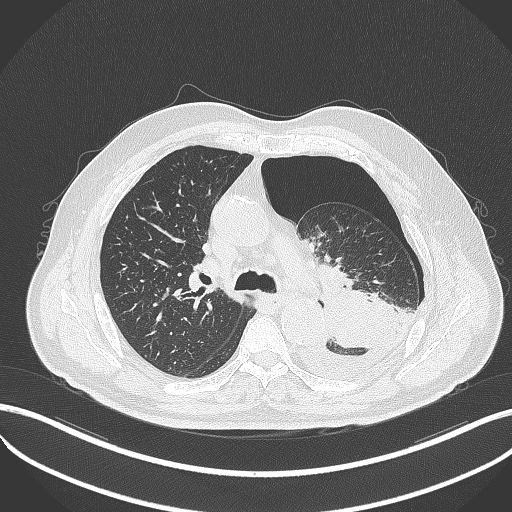
Chest CT, one axial slice; slice 337 of 464 in the series (ordered by position); reconstruction kernel B70f; 120 kVp; lung window (W 1500 / L -600 HU); 512 × 512 image matrix, field of view 400 × 400 mm. Male patient, age 76 years. From the clinical record (not read from this slice): clinical TNM (as recorded): T3 N0 M1b.
Structures marked on this image (rectangle marked by the reading radiologist):
- lung tumour (recorded histology: adenocarcinoma): bounding box (x1, y1, x2, y2) in pixels: (321, 271, 402, 352)